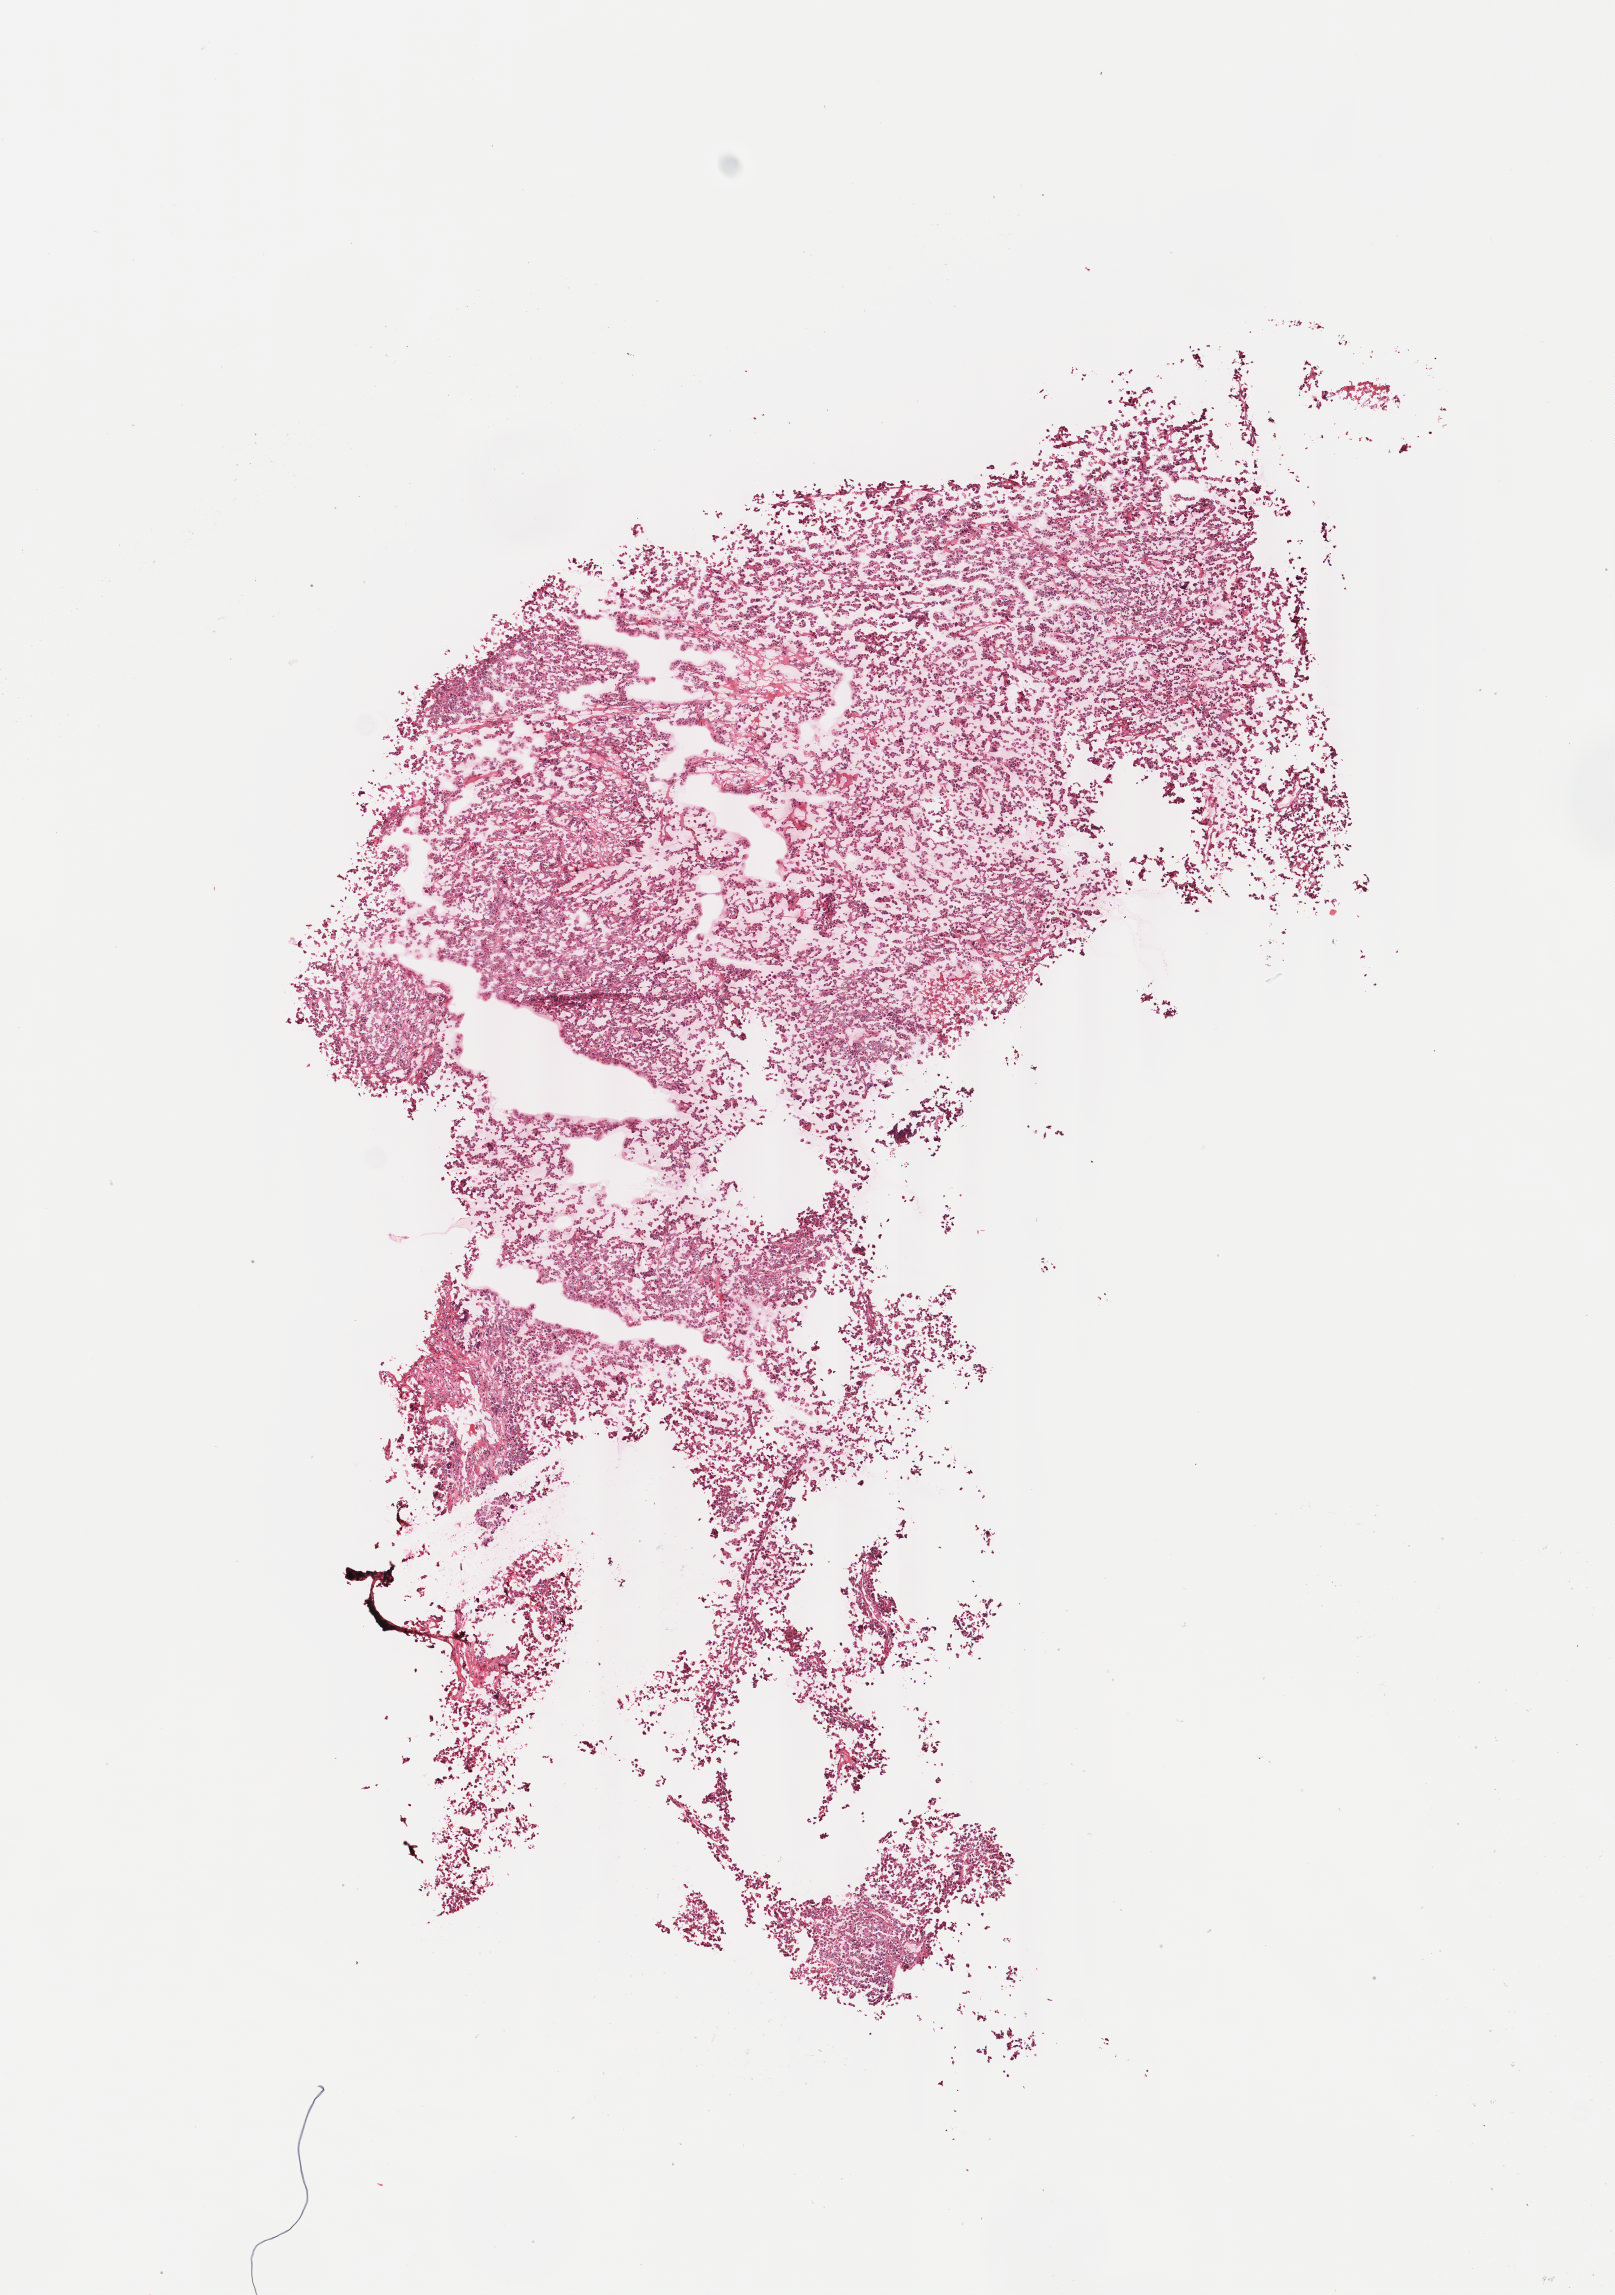
Digitized Hematoxylin and eosin (H&E) stained tissue section (whole slide) — whole scanned area (about 6.4 x 9.1 mm, from a 40x scan) shown as a low-resolution overview; frozen section from the top of the tissue portion; sample: primary tumour, adrenal cortex. Male patient; age at initial diagnosis 52 years. Slide review estimates, as recorded: tumour cells 99%, tumour nuclei 99%, normal cells 0%, stromal cells 1%, necrosis 0%. Infiltration values recorded for this section: lymphocyte infiltration 0%, monocyte infiltration 0%, neutrophil infiltration 0%.
Histologic diagnosis: Adrenal cortical carcinoma (cortex of adrenal gland).